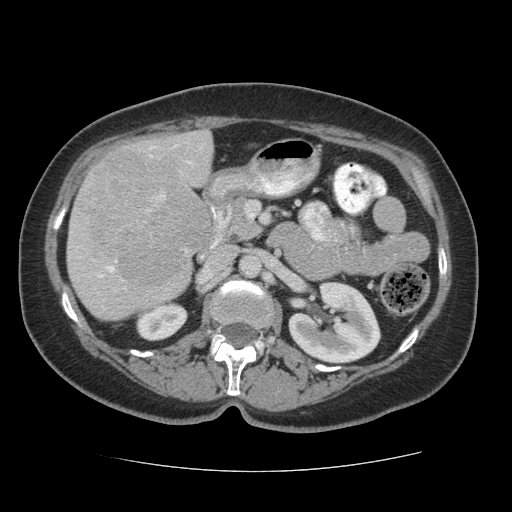
Contrast-enhanced abdominal CT (liver protocol), one axial slice; position 24 of 75 along the scan axis; 140 kVp; soft-tissue window (W 400 / L 40 HU); 512 × 512 image matrix, field of view 360 × 360 mm. From the clinical record (not read from this slice): diagnosis: hepatocellular carcinoma (patient treated with transarterial chemoembolisation; whether this scan precedes or follows treatment is not stated here); TNM stage (as recorded): Stage-I; Child-Pugh class: A; tumour nodularity: uninodular.
Outlined on this slice (semi-automatically segmented with operator editing):
- liver parenchyma outside the tumour (the mass and vessels are separate outlines, so this box may not span the whole liver): bounding box (x1, y1, x2, y2) in pixels: (66, 130, 212, 320)
- mass: (70, 147, 213, 299)
- liver vessels: (97, 145, 203, 278)